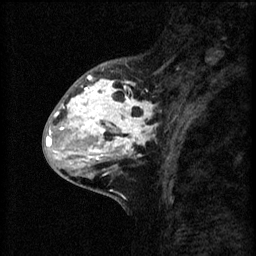
Breast MRI (dynamic contrast-enhanced), one sagittal slice. Position 23 of 60 along the scan axis. 3 images stored at this slice position (order not interpretable as contrast timing). 1.5 T. TE 4.2 ms, TR 8.2 ms. 2 mm slice thickness. 256 × 256 image matrix, field of view 180 × 180 mm. Female patient, age 41 years.
Annotated regions visible in this slice (semi-automatic segmentation, software-assisted and operator-edited):
- analysis volume of interest (the breast-tissue region the enhancement analysis was run in; not a lesion): box from (x=53, y=62) to (x=159, y=175) px
- tumour enhancement mask (voxels above the 70 % enhancement threshold inside the analysis volume of interest): (x=54, y=76)–(x=158, y=175)